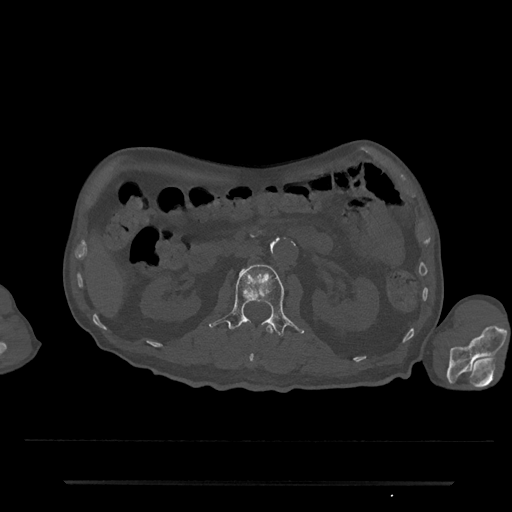
CT including the spine, one axial slice. Position 77 of 797 along the scan axis. Reconstruction kernel Br40s/3. 120 kVp. Bone window (W 1800 / L 400 HU). 0.5 mm slice thickness. 512 × 512 image matrix, field of view 427 × 427 mm. Patient: male, 74 years. Case-level facts recorded for this patient, not image findings: primary cancer: prostate.
Annotated regions visible in this slice (semi-automatically segmented with operator editing):
- L1 vertebra: bounding box (x1, y1, x2, y2) in pixels: (248, 325, 274, 365)
- L2 vertebra: (209, 264, 304, 337)